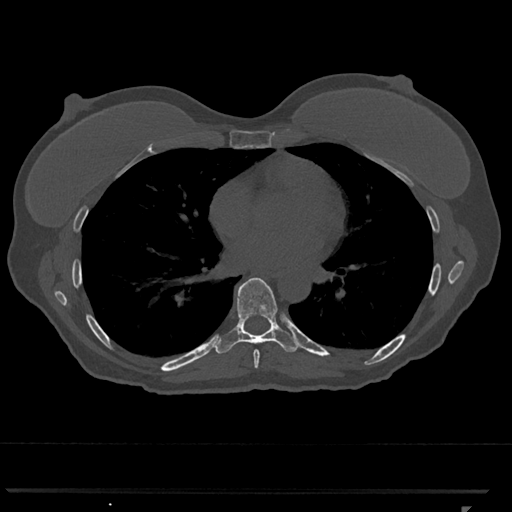
CT including the spine, one axial slice; slice 674 of 793 in the series (ordered by position); reconstruction kernel Br40s/3; bone window (W 1800 / L 400 HU); 0.5 mm slice thickness; 512 × 512 image matrix. Female patient, age 62 years. Case-level facts recorded for this patient, not image findings: primary cancer: renal.
Structures marked on this image (semi-automatically segmented with operator editing):
- T7 vertebra: bounding box (x1, y1, x2, y2) in pixels: (253, 350, 260, 368)
- T8 vertebra: (214, 277, 299, 354)